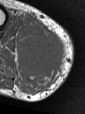
MRI of an extremity soft-tissue mass, one axial slice; position 30 of 47 along the scan axis; MR volume resampled by the dataset authors to the PET/CT grid (not the native acquisition matrix); 3.27 mm slice thickness; 85 × 114 image matrix, field of view 83 × 111 mm. Male patient. From the clinical record (not read from this slice): histological type: pleiomorphic liposarcoma; grade: high; site of the primary tumour: right calf.
Structures marked on this image (expert contour drawn on MRI and transferred to this co-registered scan by the dataset authors):
- gross tumour volume including surrounding oedema: bounding box [x1, y1, x2, y2] px = [20, 25, 66, 79]
- gross tumour volume (mass): [24, 34, 66, 74]